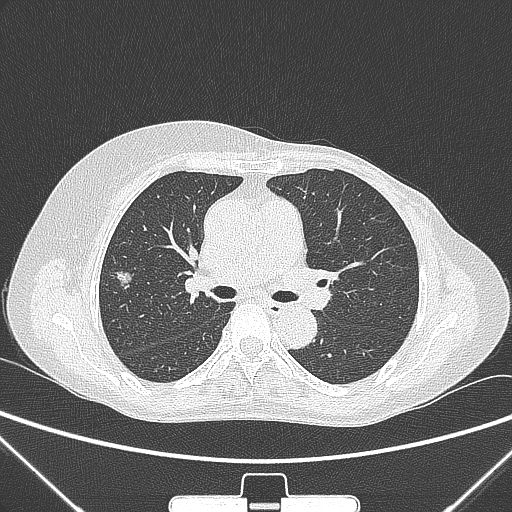
Chest CT, one axial slice; position 153 of 265 along the scan axis; 120 kVp; lung window (W 1500 / L -600 HU); 512 × 512 image matrix, field of view 350 × 350 mm. Female patient, age 64 years. Case-level facts recorded for this patient, not image findings: clinical TNM (as recorded): T1c N0 M0.
Annotated regions visible in this slice (bounding box drawn by a radiologist):
- lung tumour (recorded histology: adenocarcinoma): bounding box (x1, y1, x2, y2) in pixels: (113, 262, 137, 297)